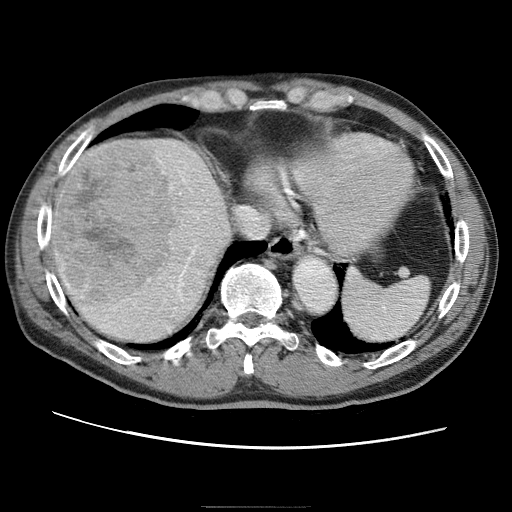
Contrast-enhanced abdominal CT (liver protocol), one axial slice. Position 56 of 75 along the scan axis. Reconstruction kernel STANDARD. 120 kVp. One of 2 acquisitions stored at this slice position. Soft-tissue window (W 400 / L 40 HU). 2.5 mm slice thickness. 512 × 512 image matrix. From the clinical record (not read from this slice): diagnosis: hepatocellular carcinoma (patient treated with transarterial chemoembolisation; whether this scan precedes or follows treatment is not stated here); TNM stage (as recorded): Stage-II.
Outlined on this slice (semi-automatically segmented with operator editing):
- abdominal aorta: box from (x=294, y=257) to (x=334, y=311) px
- liver parenchyma outside the tumour (the mass and vessels are separate outlines, so this box may not span the whole liver): (x=48, y=136)–(x=236, y=344)
- mass: (x=55, y=141)–(x=184, y=302)
- liver vessels: (x=63, y=139)–(x=229, y=307)